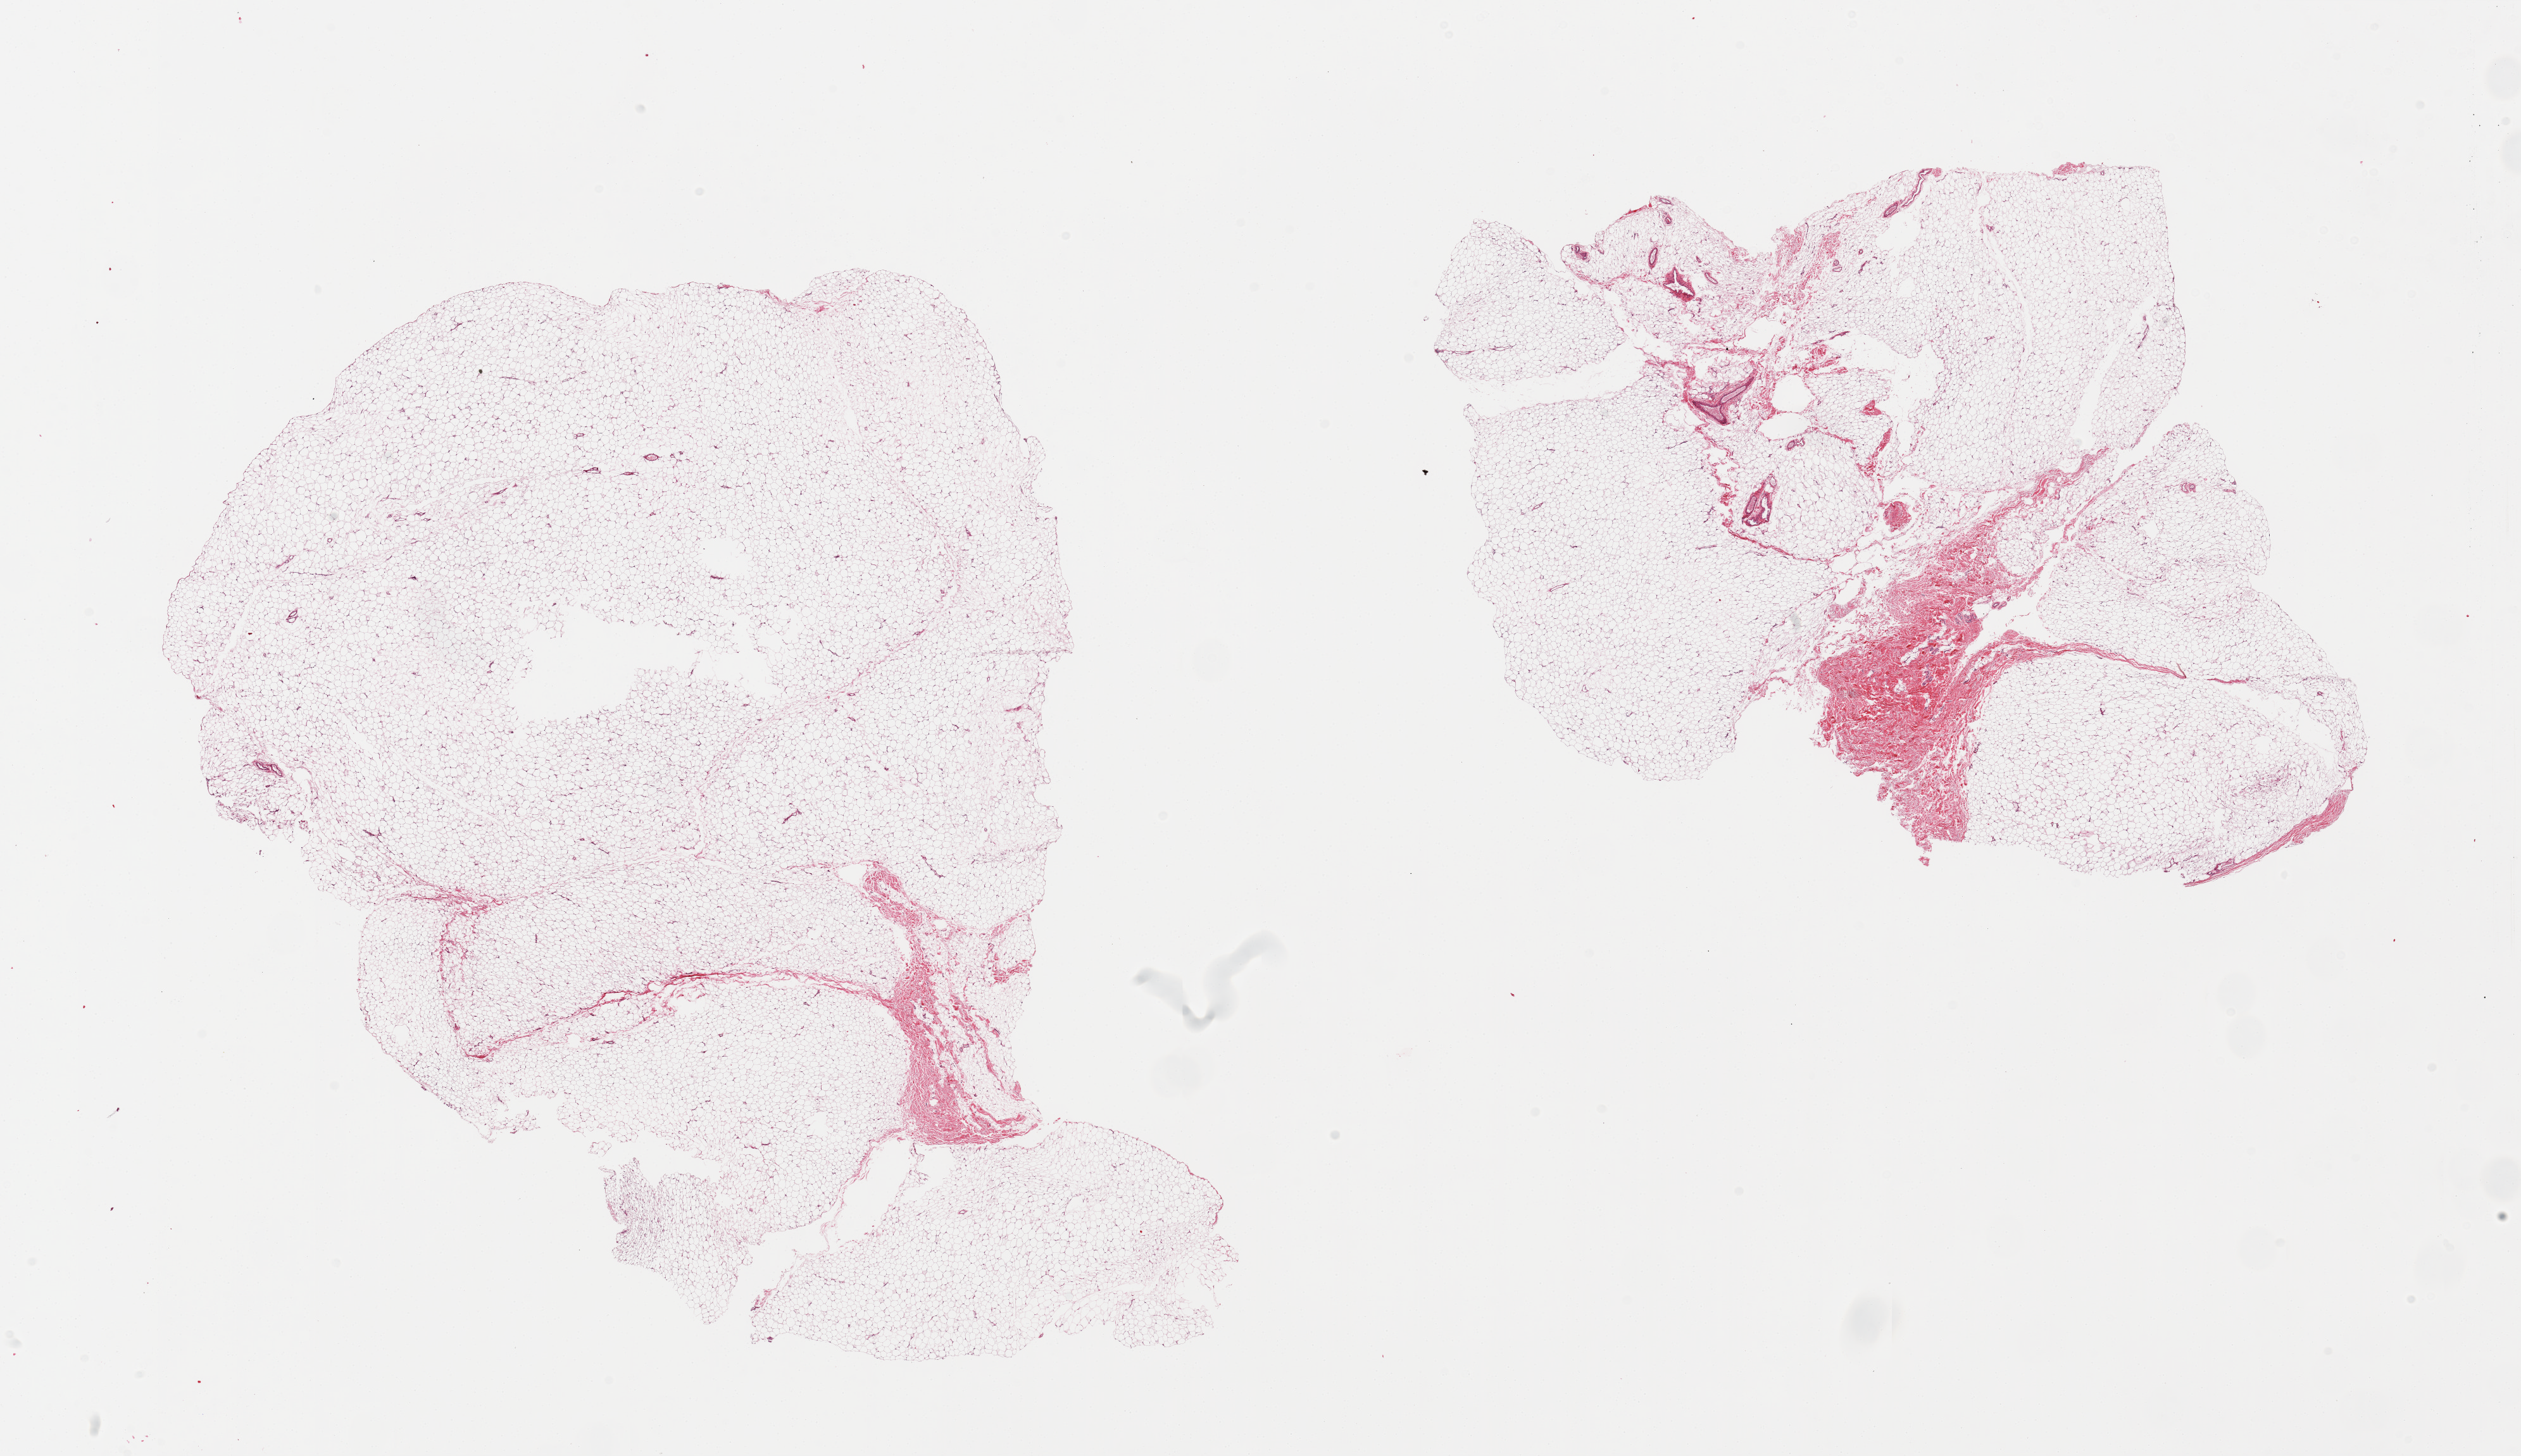
H&E whole-slide image — low-resolution overview of the scanned area, about 31.5 x 18.2 mm. PAXgene-fixed paraffin-embedded (PFPE) section. Sampled site (target tissue): breast. Donor tissue sample. Male donor.
Pathologist's review note for this sample: 2 pieces; predominantly fat with 5-15% fibrous tissue, no ductal elements seen.